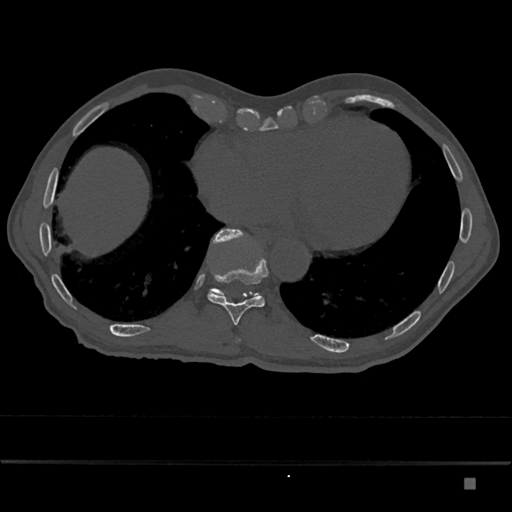
CT including the spine, one axial slice. Bone window (W 1800 / L 400 HU). 512 × 512 image matrix, field of view 390 × 390 mm. Male patient, age 72 years. From the clinical record (not read from this slice): primary cancer: prostate.
Annotated regions visible in this slice (semi-automatic segmentation, software-assisted and operator-edited):
- T10 vertebra: box from (x=207, y=258) to (x=269, y=325) px
- T11 vertebra: (x=209, y=229)–(x=259, y=299)